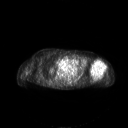
FDG PET of an extremity soft-tissue mass (from a PET/CT study), one axial slice; 3.27 mm slice thickness; 128 × 128 image matrix, field of view 700 × 700 mm. Female patient, age 83 years. From the clinical record (not read from this slice): histological type: pleiomorphic leiomyosarcoma; grade: high; site of the primary tumour: left biceps.
Annotated regions visible in this slice (expert contour drawn on MRI and transferred to this co-registered scan by the dataset authors):
- gross tumour volume including surrounding oedema: bounding box [x1, y1, x2, y2] px = [90, 60, 106, 77]
- gross tumour volume (mass): [90, 60, 106, 77]